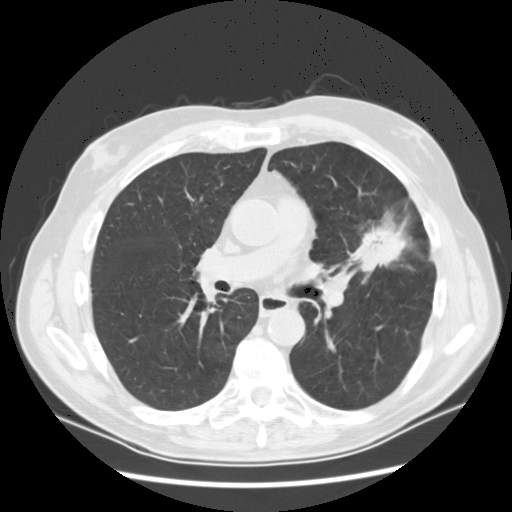
Axial slice from a low-dose chest CT screening exam, baseline screening round, lung window (W 1500 / L -600 HU), 2.5 mm slice thickness, 120 kVp. Male participant, aged 65 years at enrolment. Current smoker at enrolment.
Lesion marked by an expert reader, bounding box (x1, y1, x2, y2) in pixels: (348, 210, 415, 279). Screening reader's record for this exam (one nodule recorded; not confirmed to be the boxed lesion): non-calcified nodule or mass ≥4 mm, left upper lobe, 37 × 27 mm, spiculated (stellate) margins, soft tissue attenuation. Official screen result: positive, change unspecified: nodule(s) >= 4 mm or enlarging nodule(s), mass(es), or other non-specific abnormalities suspicious for lung cancer. Participant outcome: lung cancer diagnosed 56 days after this screen — non-small cell carcinoma, poorly differentiated (G3), stage IA (AJCC 6th edition).